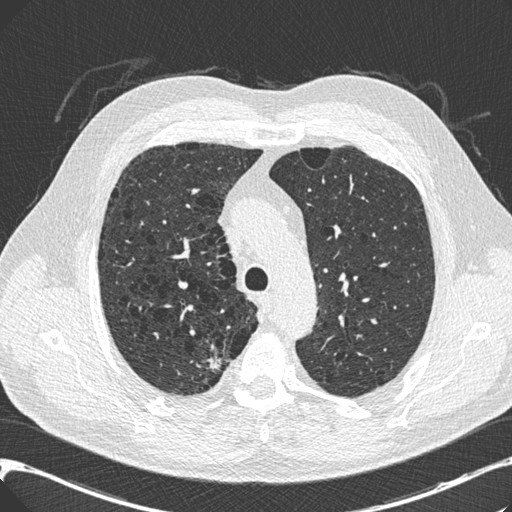
Axial slice from a low-dose chest CT screening exam, third annual screen, lung window (W 1500 / L -600 HU), 0.75 mm slice thickness, standard (soft-tissue) reconstruction kernel (B30f), 512 × 512 image matrix. Male participant, aged 68 years at enrolment. Current smoker at enrolment.
• Expert-annotated lung lesion, box from (x=189, y=345) to (x=236, y=382) px.
• The screening reader recorded 3 non-calcified nodules or masses ≥4 mm on this exam (right upper lobe, right upper lobe, left lower lobe); which of them this box marks is not recorded.
• Later outcome: lung cancer diagnosed 46 days after this screen — adenocarcinoma, NOS, right upper lobe, well differentiated (G1), stage IB (AJCC 6th edition), 15 mm at pathology.